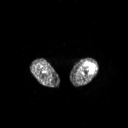
FDG PET of an extremity soft-tissue mass (from a PET/CT study), one axial slice. Slice 195 of 267 in the series (ordered by position). 128 × 128 image matrix, field of view 700 × 700 mm. Patient: female, 62 years. From the clinical record (not read from this slice): histological type: undifferentiated – high grade; grade: high; site of the primary tumour: left thigh.
Outlined on this slice (expert contour drawn on MRI and transferred to this co-registered scan by the dataset authors):
- gross tumour volume including surrounding oedema: bounding box [x1, y1, x2, y2] px = [85, 63, 95, 72]